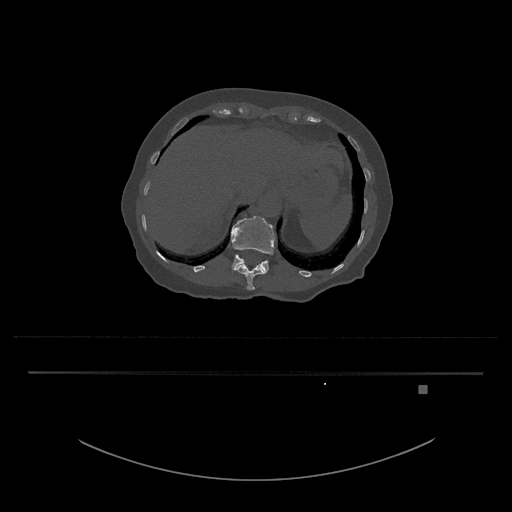
CT including the spine, one axial slice. Slice 583 of 797 in the series (ordered by position). Reconstruction kernel Br40s/3. Bone window (W 1800 / L 400 HU). 0.5 mm slice thickness. 512 × 512 image matrix. Female patient, age 57 years. From the clinical record (not read from this slice): primary cancer: cervical.
Structures marked on this image (semi-automatically segmented with operator editing):
- L1 vertebra: bounding box [x1, y1, x2, y2] px = [231, 216, 276, 273]
- T12 vertebra: [234, 262, 265, 290]